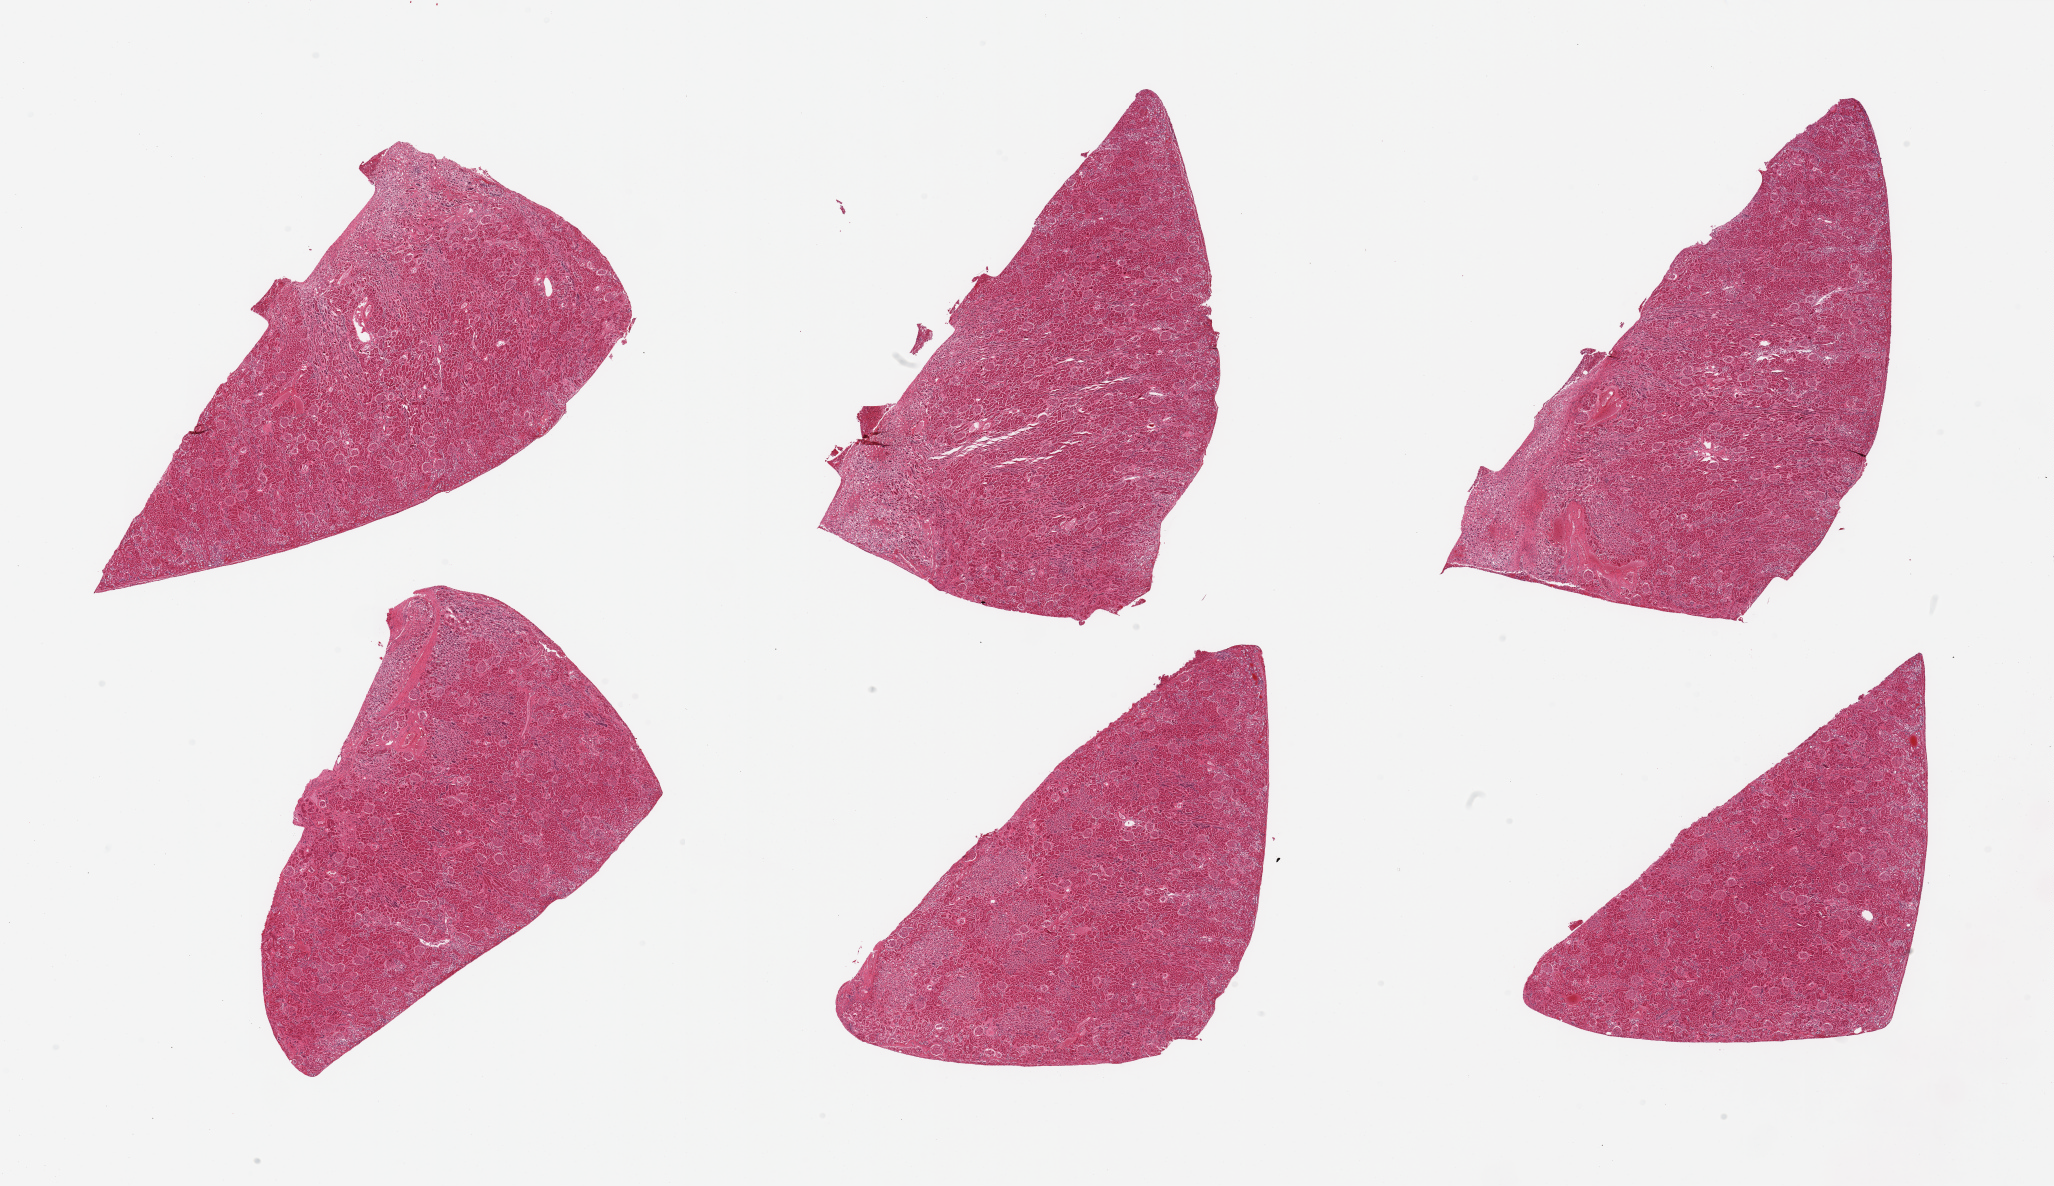
Digitized H&E-stained section, brightfield — low-resolution overview of the scanned area, about 32.5 x 18.8 mm; PAXgene-fixed paraffin-embedded (PFPE) section; target tissue: renal cortex; tissue donor sample.
Reviewer comment on this tissue sample: 6 pieces; glomeruli in all pieces.